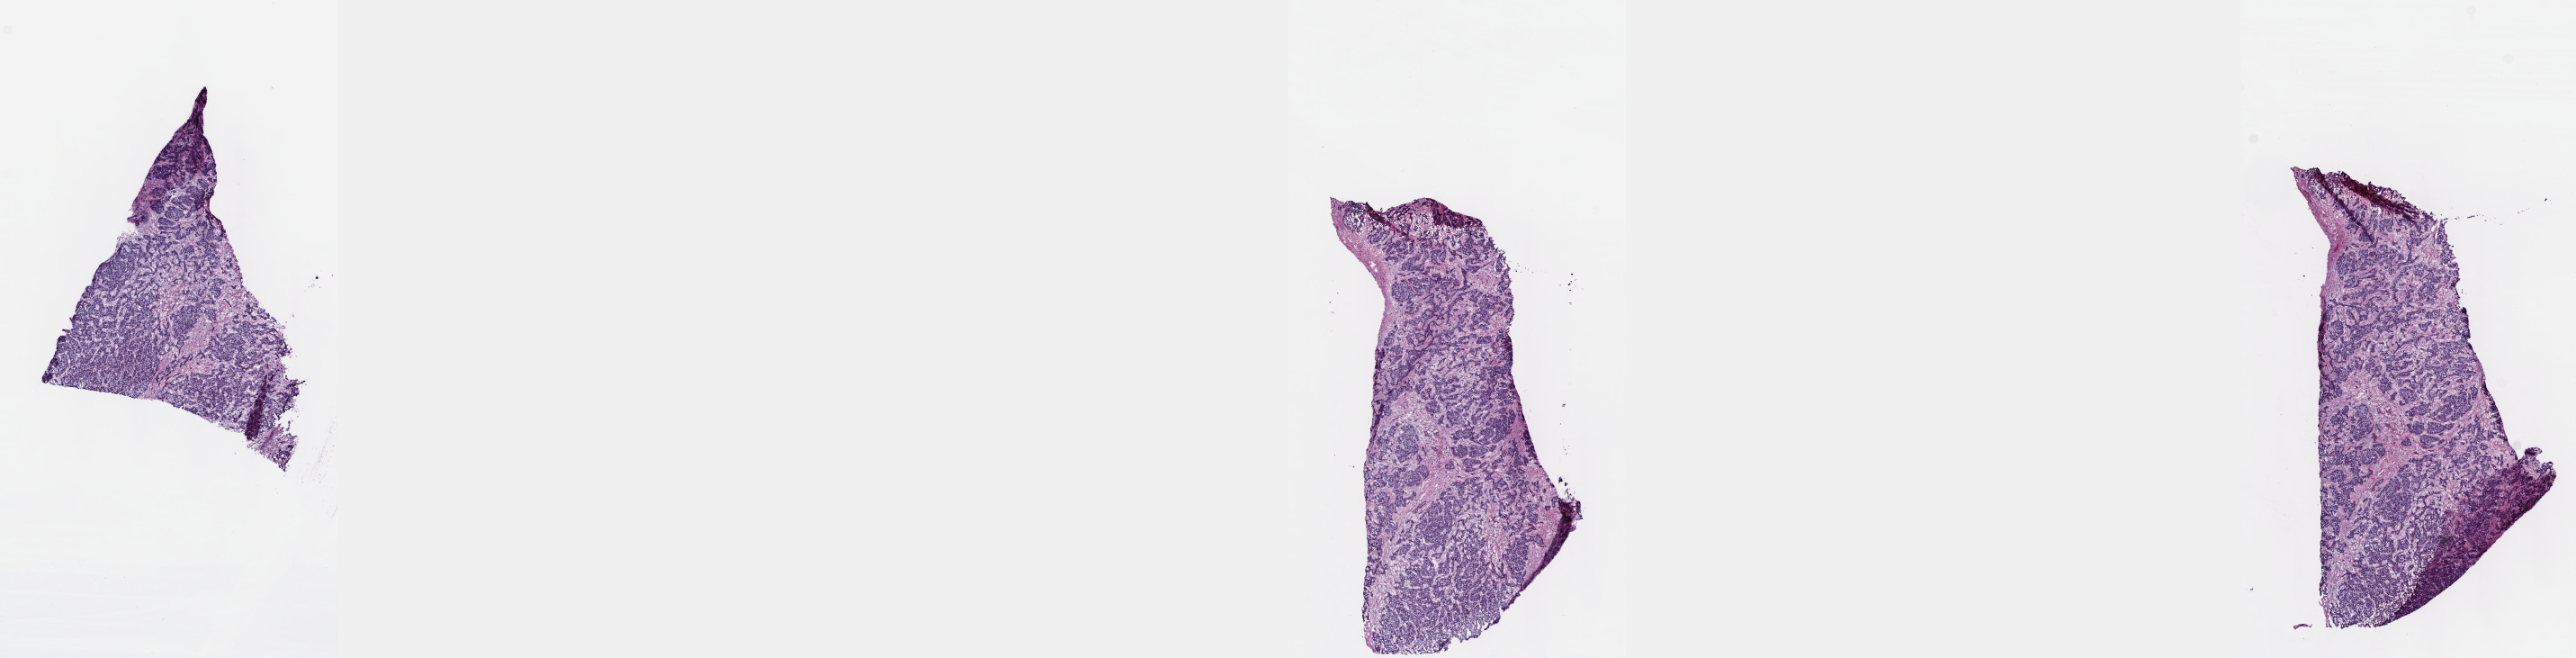
Digitized Hematoxylin and eosin (H&E) stained tissue section (whole slide) — whole scanned area (about 23.1 x 5.9 mm) shown as a low-resolution overview. Frozen section from the top of the tissue portion. Primary tumour sample from the liver. Patient: female, age at initial diagnosis 59 years. Histologic grade: G3 (poorly differentiated). Pathologist review of this section (percent, as recorded): tumour cells 75%, tumour nuclei 75%, normal cells 0%, stromal cells 25%, necrosis 0%. Infiltration values recorded for this section: lymphocyte infiltration 3%, monocyte infiltration 1%, neutrophil infiltration 2%.
Pathologic diagnosis: Hepatocellular carcinoma, NOS. AJCC pathologic stage: I (7th edition). TNM: T1 N0 MX.